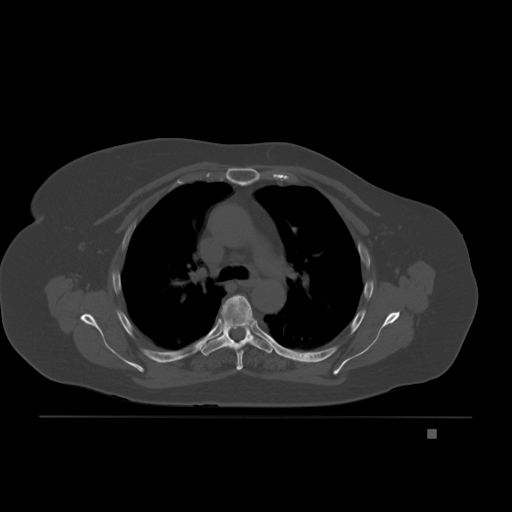
CT including the spine, one axial slice. Slice 148 of 221 in the series (ordered by position). Bone window (W 1800 / L 400 HU). 512 × 512 image matrix, field of view 474 × 474 mm. Female patient, age 63 years. From the clinical record (not read from this slice): primary cancer: breast.
Structures marked on this image (semi-automatic segmentation, software-assisted and operator-edited):
- T4 vertebra: bounding box (x1, y1, x2, y2) in pixels: (222, 295, 253, 370)
- T5 vertebra: (201, 324, 273, 356)